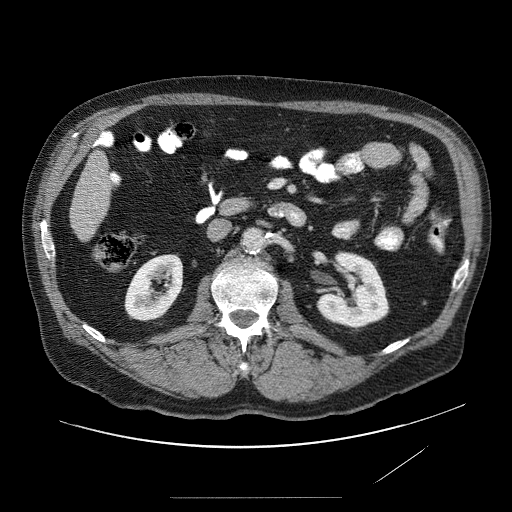
Contrast-enhanced abdominal CT (liver protocol), one axial slice. Position 10 of 89 along the scan axis. 120 kVp. Soft-tissue window (W 400 / L 40 HU). 2.5 mm slice thickness. 512 × 512 image matrix. From the clinical record (not read from this slice): diagnosis: hepatocellular carcinoma (patient treated with transarterial chemoembolisation; whether this scan precedes or follows treatment is not stated here); TNM stage (as recorded): Stage-IVA.
Annotated regions visible in this slice (semi-automatically segmented with operator editing):
- liver parenchyma outside the tumour (the mass and vessels are separate outlines, so this box may not span the whole liver): bounding box <68,130,116,244> (left, top, right, bottom; pixels)
- liver vessels: <93,131,108,208>